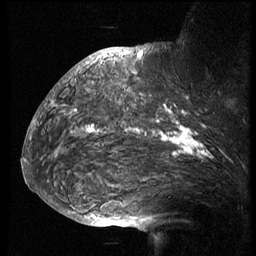
Breast MRI (dynamic contrast-enhanced), one sagittal slice. Position 48 of 74 along the scan axis. 3 images stored at this slice position (order not interpretable as contrast timing). 1.5 T. TE 4.2 ms, TR 8.9 ms. 2.5 mm slice thickness. 256 × 256 image matrix, field of view 200 × 200 mm. Patient: female, 57 years. From the clinical record (not read from this slice): setting: breast cancer imaged before/during neoadjuvant chemotherapy; receptor status: HER2-positive.
Outlined on this slice (semi-automatic segmentation, software-assisted and operator-edited):
- analysis volume of interest (the breast-tissue region the enhancement analysis was run in; not a lesion): box from (x=51, y=67) to (x=249, y=173) px
- tumour enhancement mask (voxels above the 140 % enhancement threshold inside the analysis volume of interest): (x=53, y=105)–(x=210, y=157)